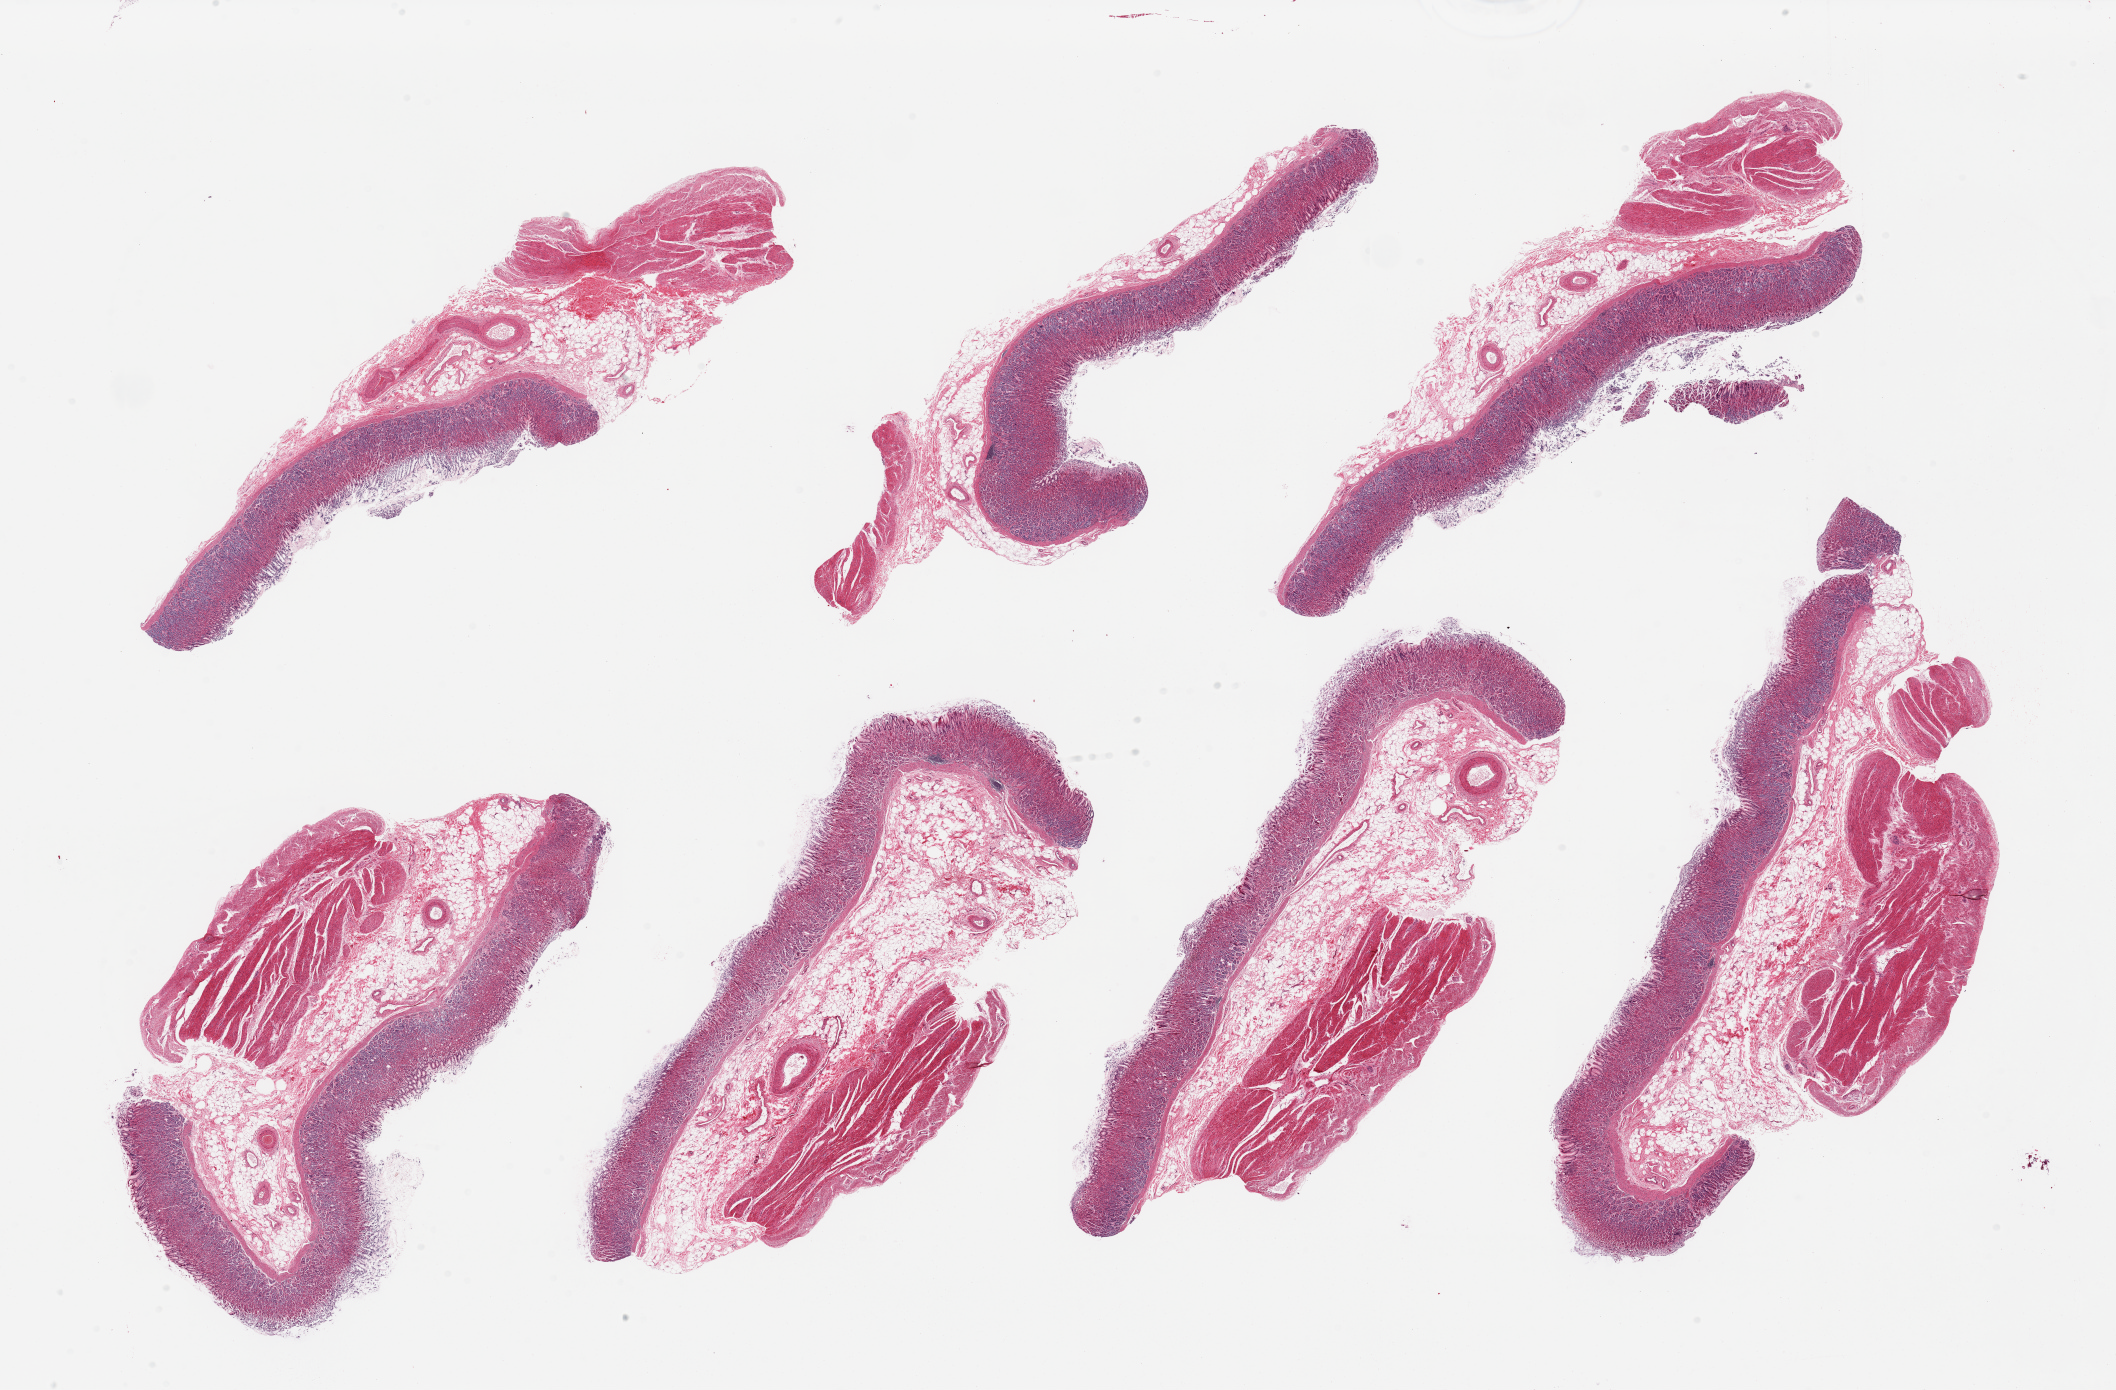
Digitized hematoxylin and eosin (H&E)-stained section, brightfield, whole scanned area (about 33.5 x 22.0 mm, acquisition: 20x scan) shown as a low-resolution overview. PAXgene-fixed, paraffin-embedded tissue. Sampled site (target tissue): stomach. Tissue donor sample.
- reviewer comment on this tissue sample: 6 pieces, mucosa well preserved, ~1mm; 25-100% thickness depending on section; valuable specimen